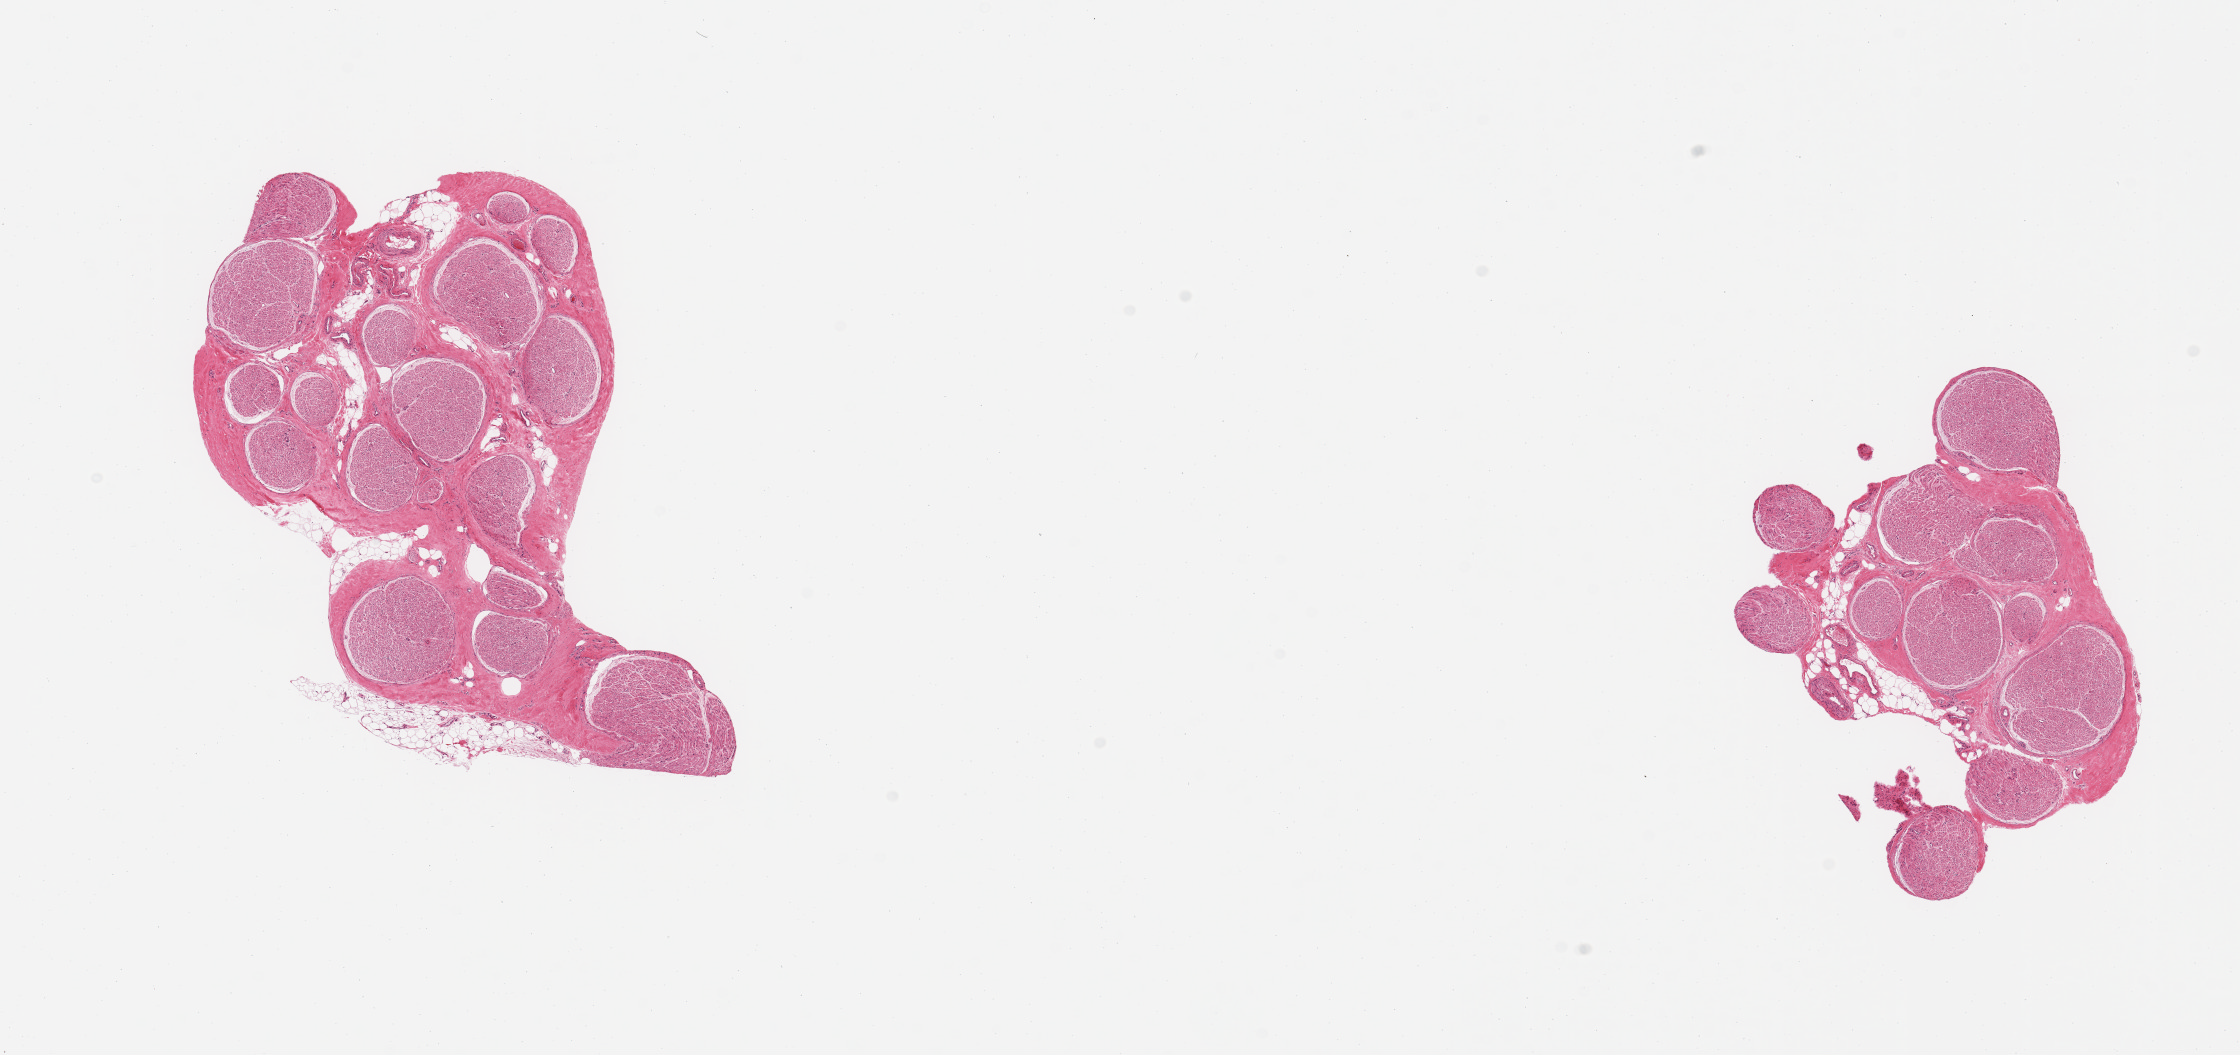
Digitized hematoxylin and eosin (H&E)-stained section, low-resolution overview of the scanned area, about 17.7 x 8.3 mm (from a 20x scan); PAXgene-fixed paraffin-embedded (PFPE) section; section of tibial nerve (target tissue); donor tissue sample.
Pathologist's review note for this sample: 2 pieces, trace adherent fat.